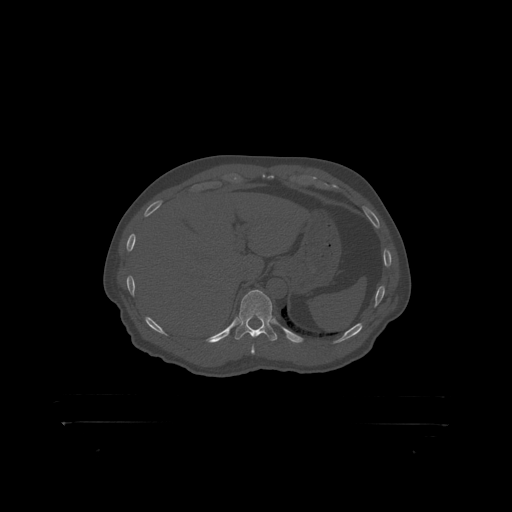
CT including the spine, one axial slice; position 381 of 399 along the scan axis; bone window (W 1800 / L 400 HU); 512 × 512 image matrix, field of view 650 × 650 mm. Patient: male, 46 years. From the clinical record (not read from this slice): primary cancer: skin.
Outlined on this slice (semi-automatically segmented with operator editing):
- T11 vertebra: bounding box <239,291,273,319> (left, top, right, bottom; pixels)